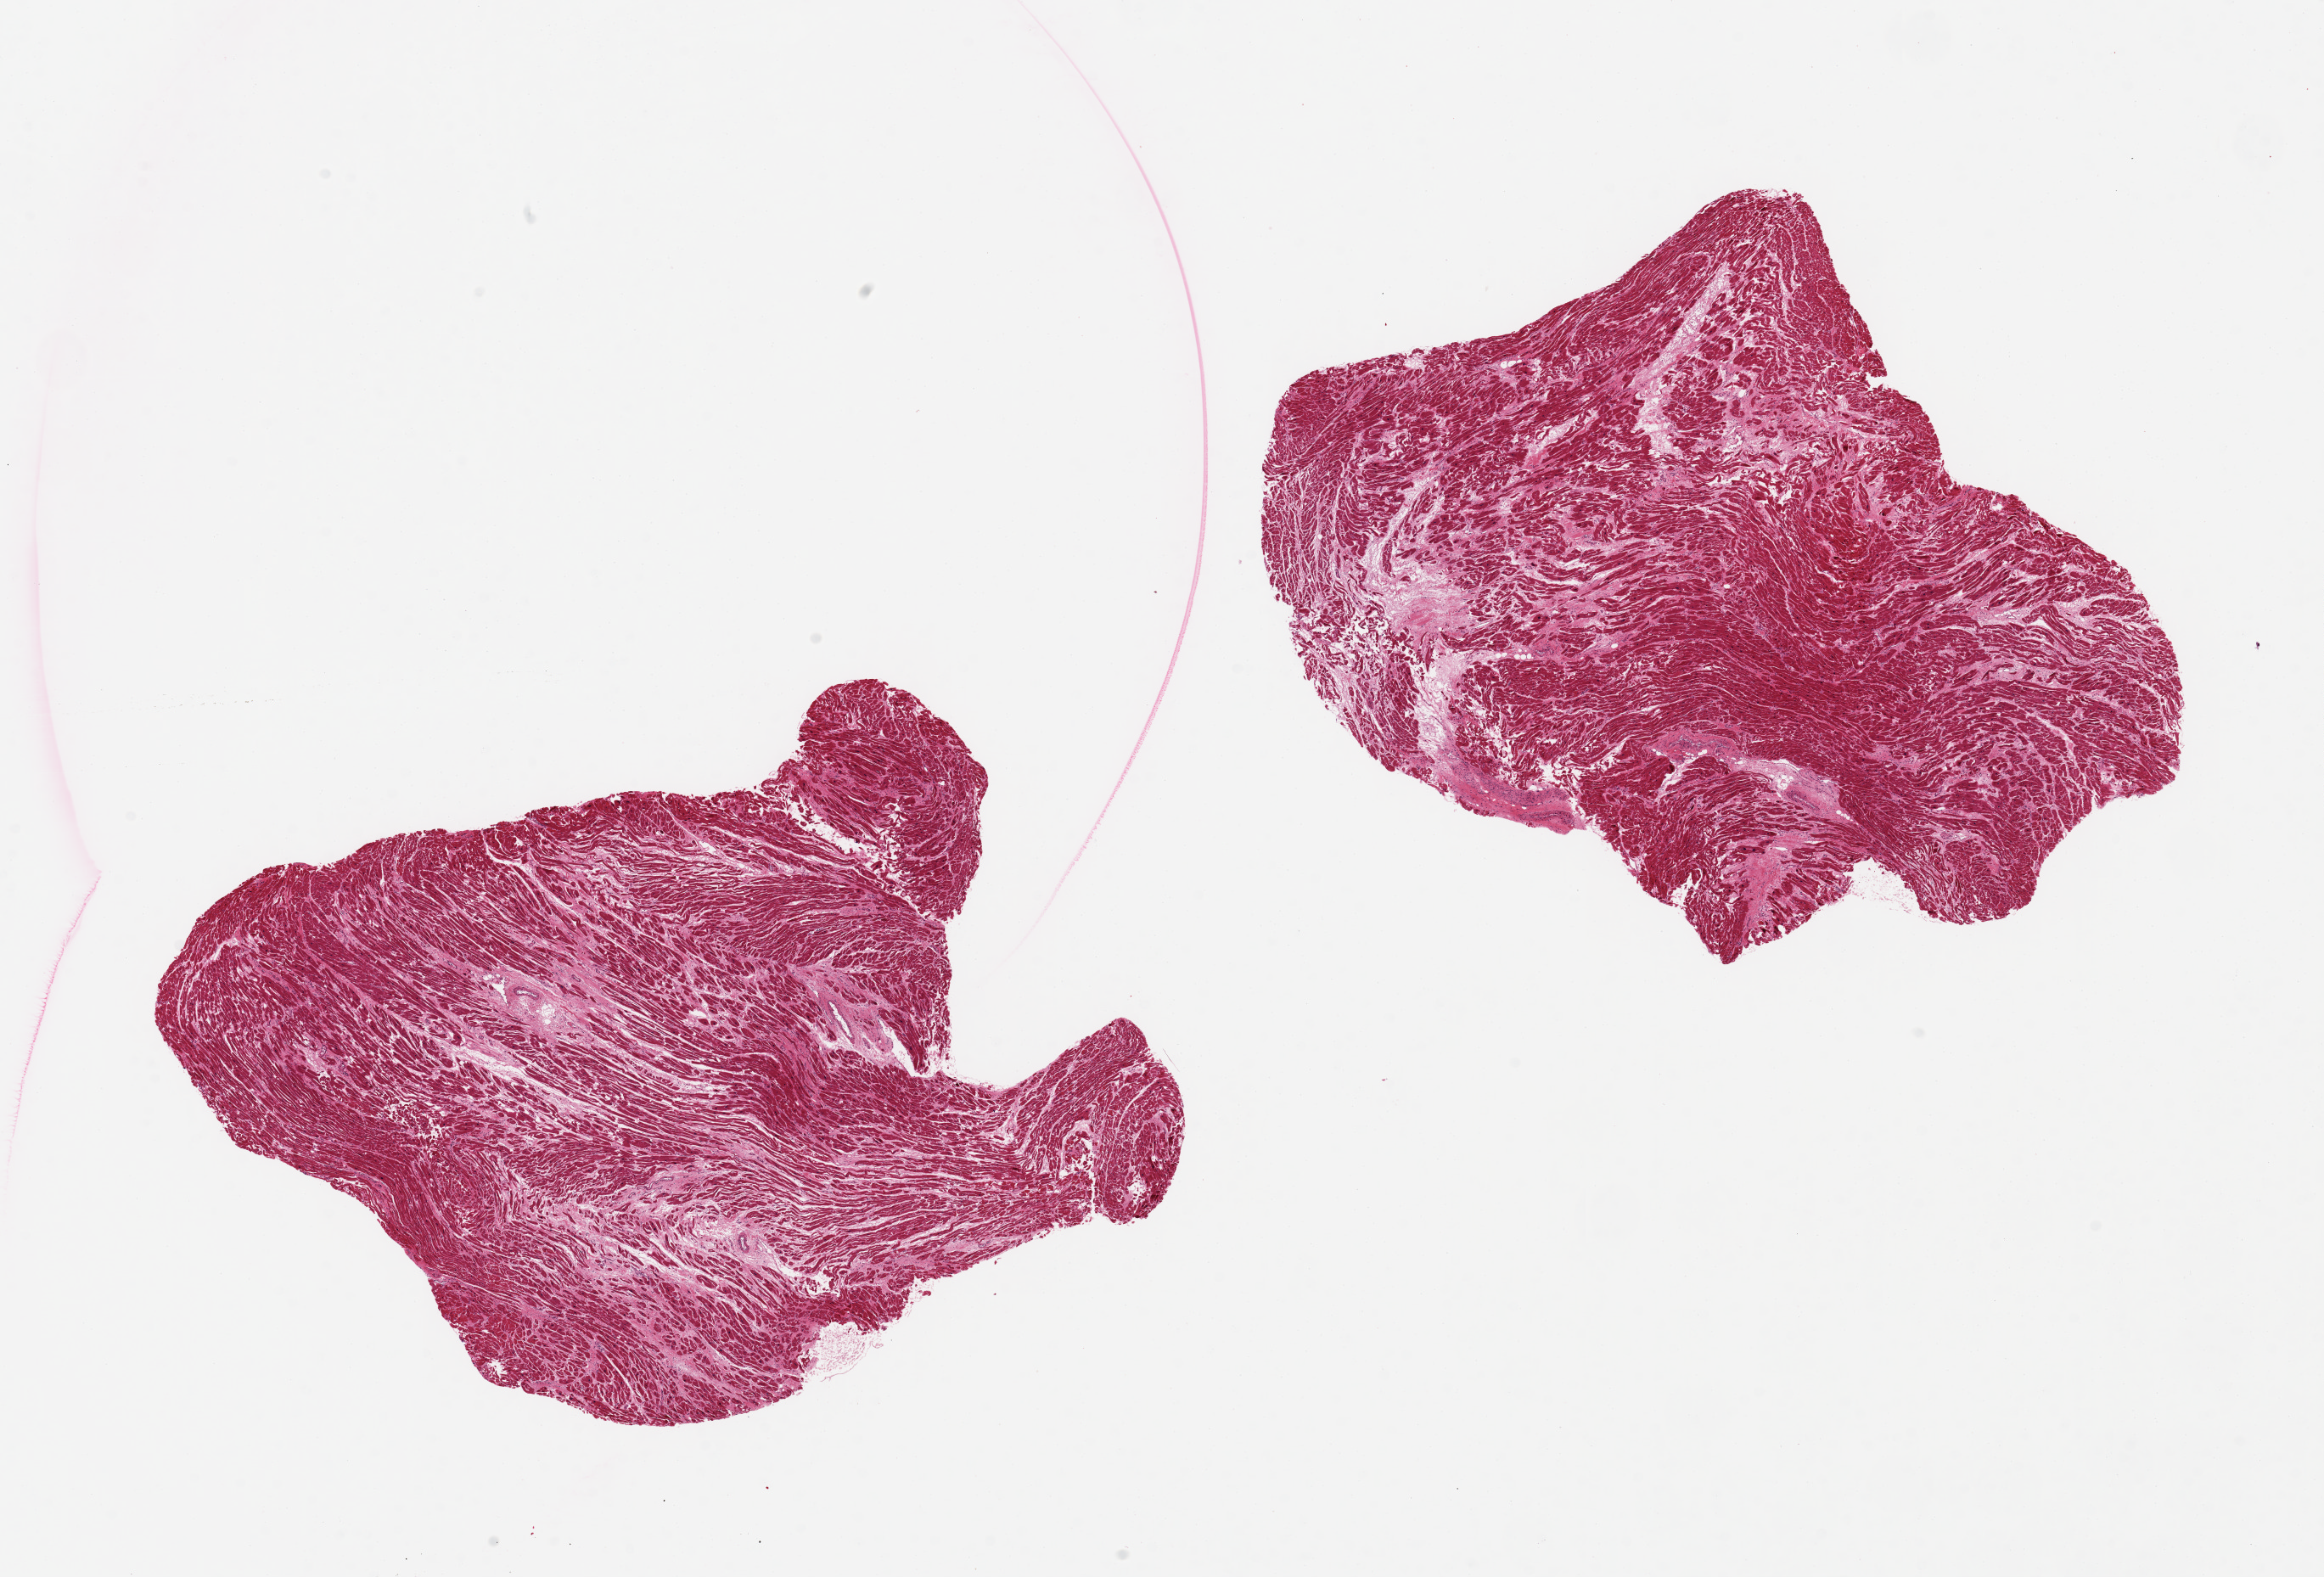
Whole-slide image, H&E stain — shown as a low-resolution overview of the whole scanned area (about 21.7 x 14.7 mm, from a 20x scan); PAXgene-fixed paraffin-embedded (PFPE) section; section of heart (target tissue); donor tissue sample. Donor sex: male.
Reviewer comment on this tissue sample: 2 pieces, 6x8 & 6x7mm; moderate patchy fibrosis, probably ischemic; enlarged nuclei.